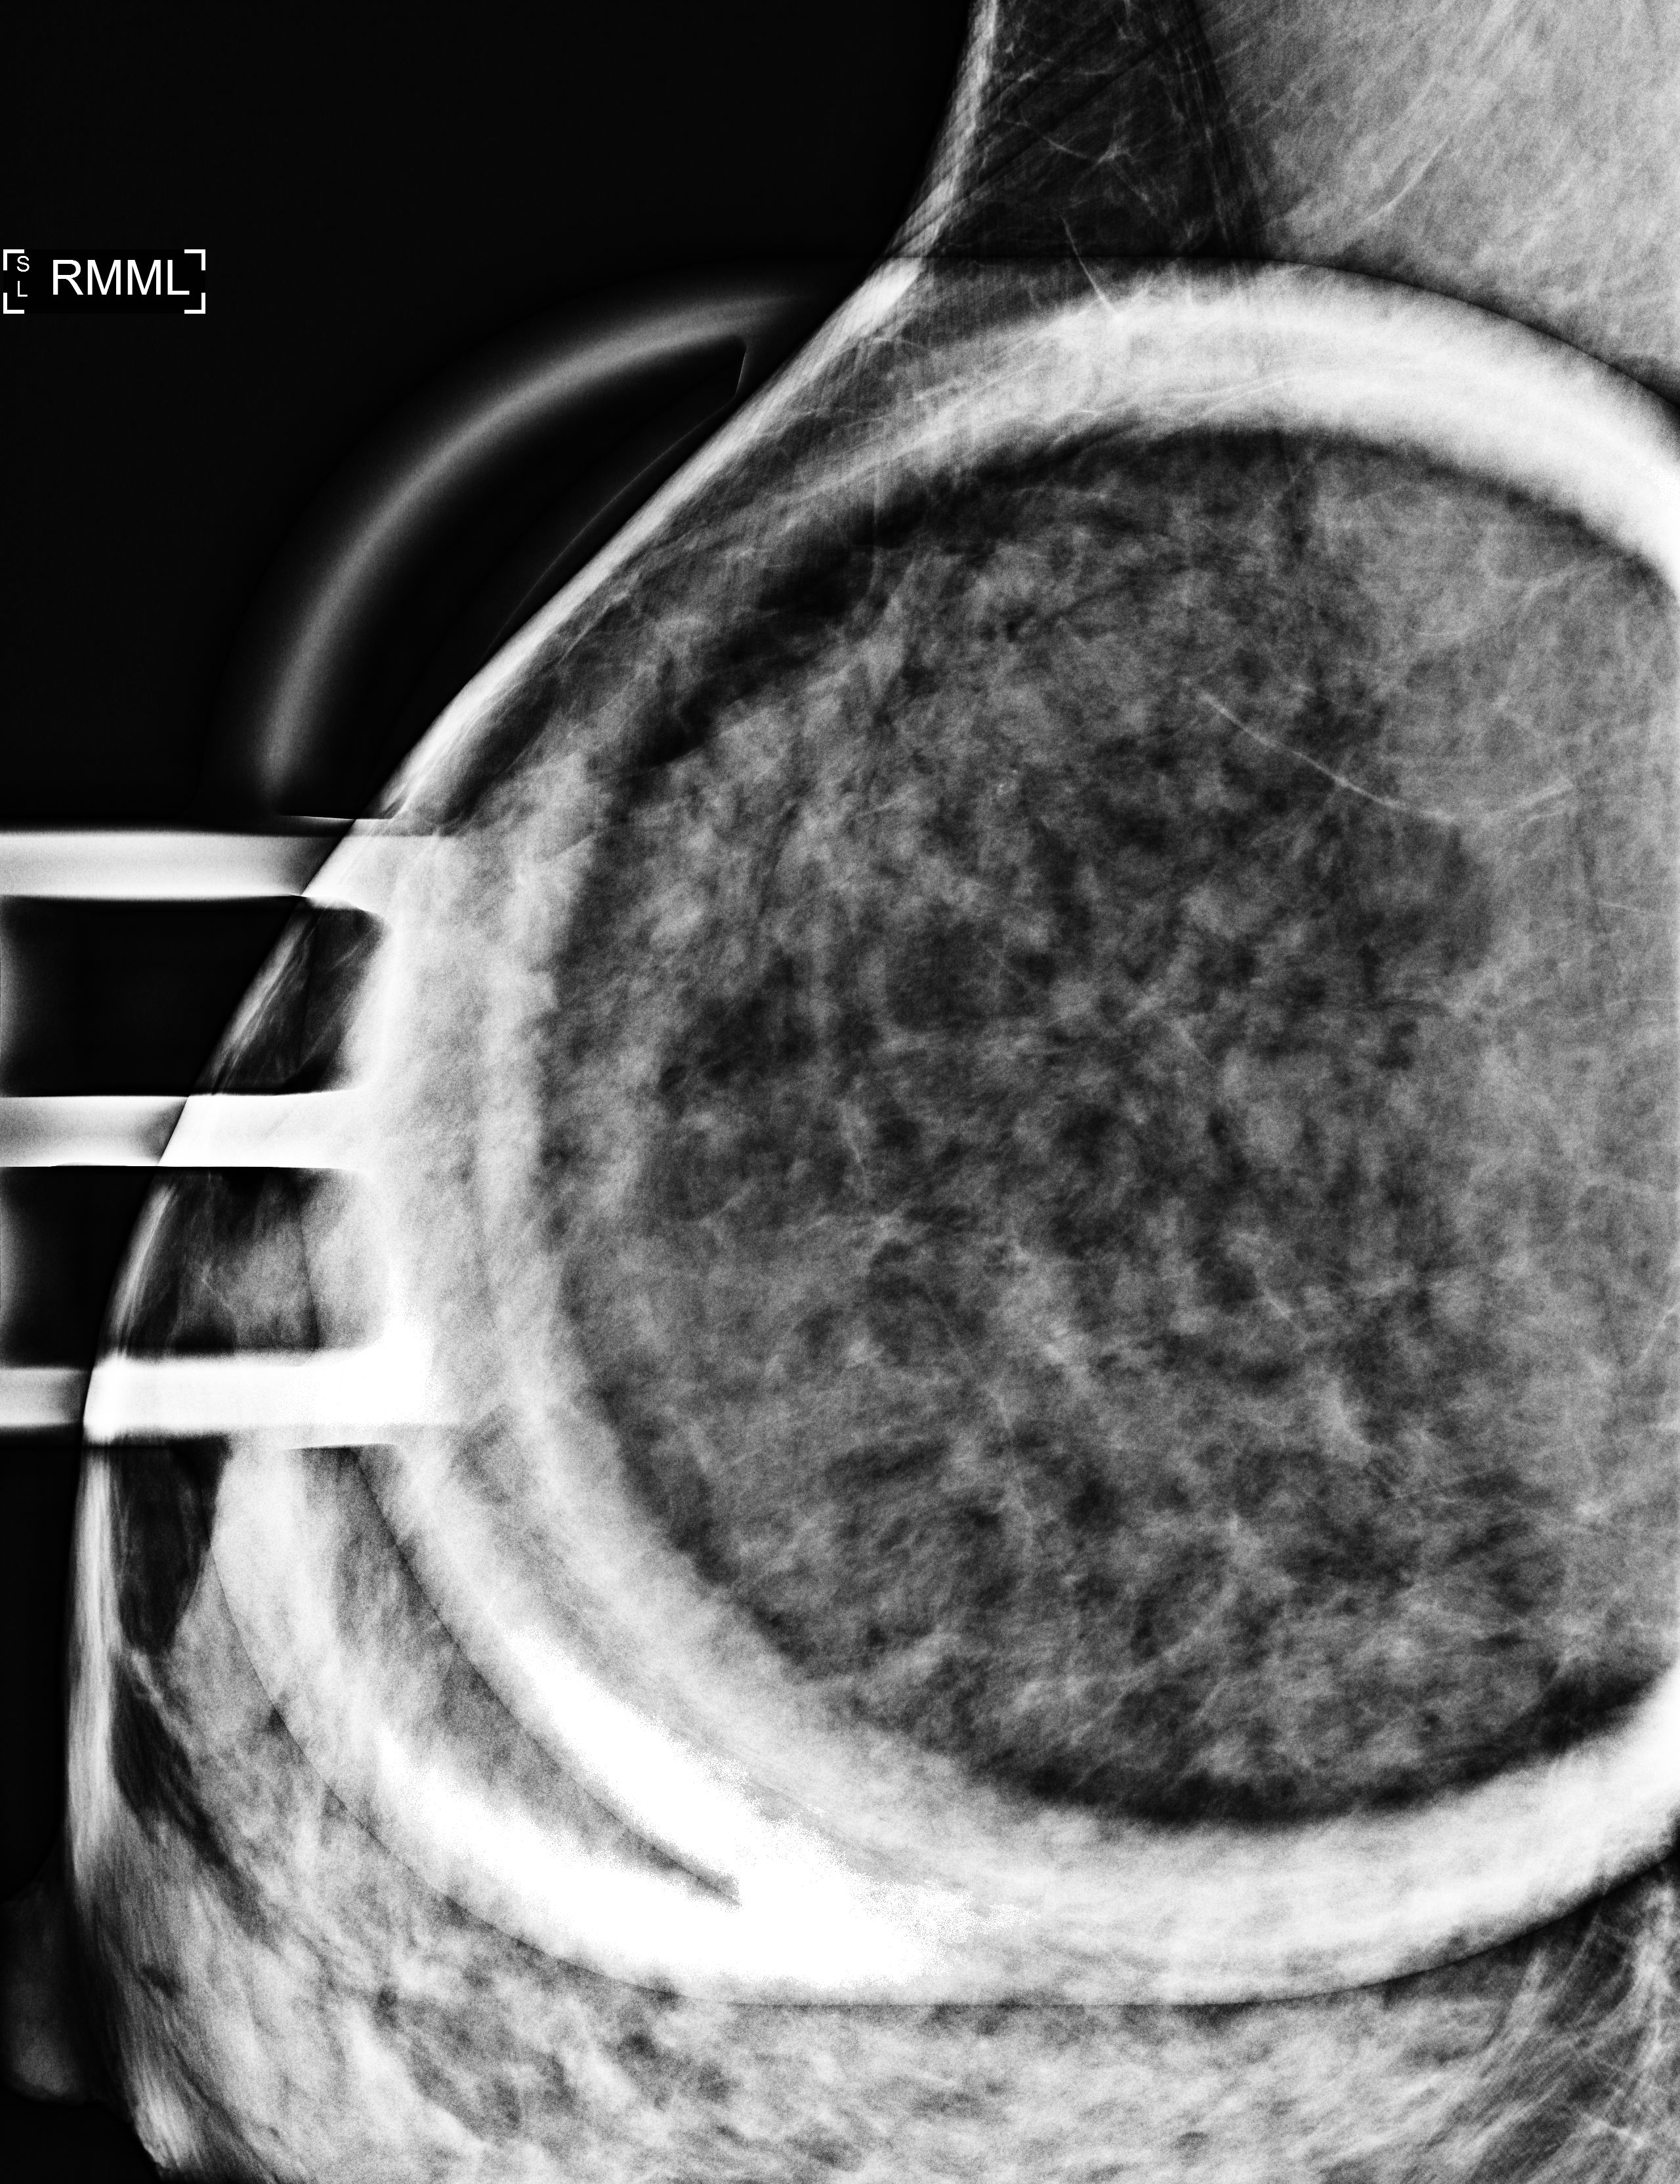
Additional work-up view, compressed breast thickness 24 mm. Patient: female, 45 years.
Image type: full-field digital mammogram. Breast: right. Projection: mediolateral (ML) view, magnification.